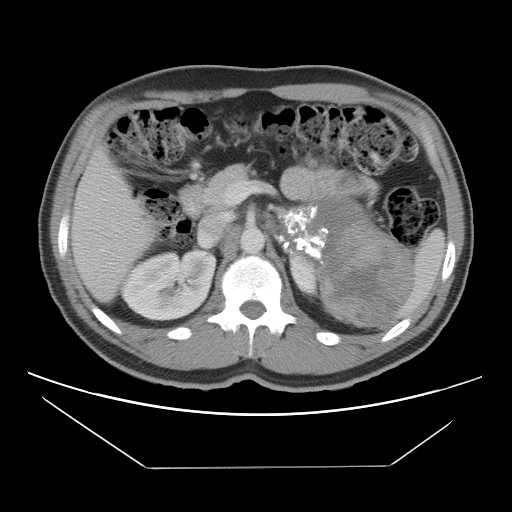
Contrast-enhanced abdominal CT, one axial slice; slice 68 of 131 in the series (ordered by position); 120 kVp; intravenous contrast given; soft-tissue window (W 400 / L 40 HU); 5 mm slice thickness; 512 × 512 image matrix, field of view 396 × 396 mm. Patient: male, 44 years. Case-level facts recorded for this patient, not image findings: diagnosis: adrenocortical carcinoma; tumour side: left adrenal; tumour size at pathology: 15.5 cm; Ki-67 index: 6 %; stage (as recorded): 2.
Structures marked on this image (semi-automatically segmented with operator editing):
- mass: bounding box [x1, y1, x2, y2] px = [281, 197, 409, 325]